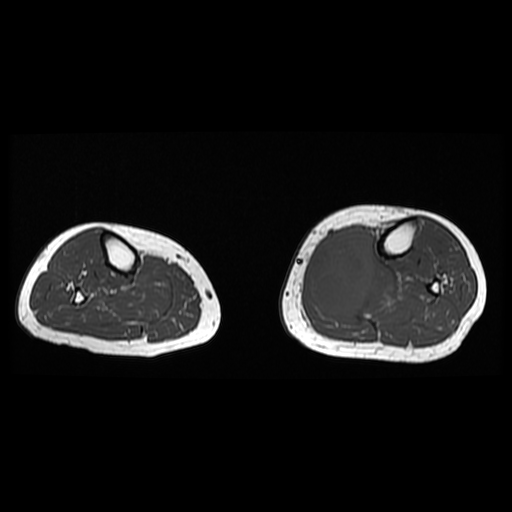
MRI of an extremity soft-tissue mass, one axial slice; position 13 of 38 along the scan axis; 512 × 512 image matrix, field of view 330 × 330 mm. Female patient. From the clinical record (not read from this slice): histological type: extraskeletal high grade osteogenic sarcoma; grade: high; site of the primary tumour: left calf.
Annotated regions visible in this slice (expert manual segmentation):
- gross tumour volume (mass): box from (x=309, y=226) to (x=375, y=315) px